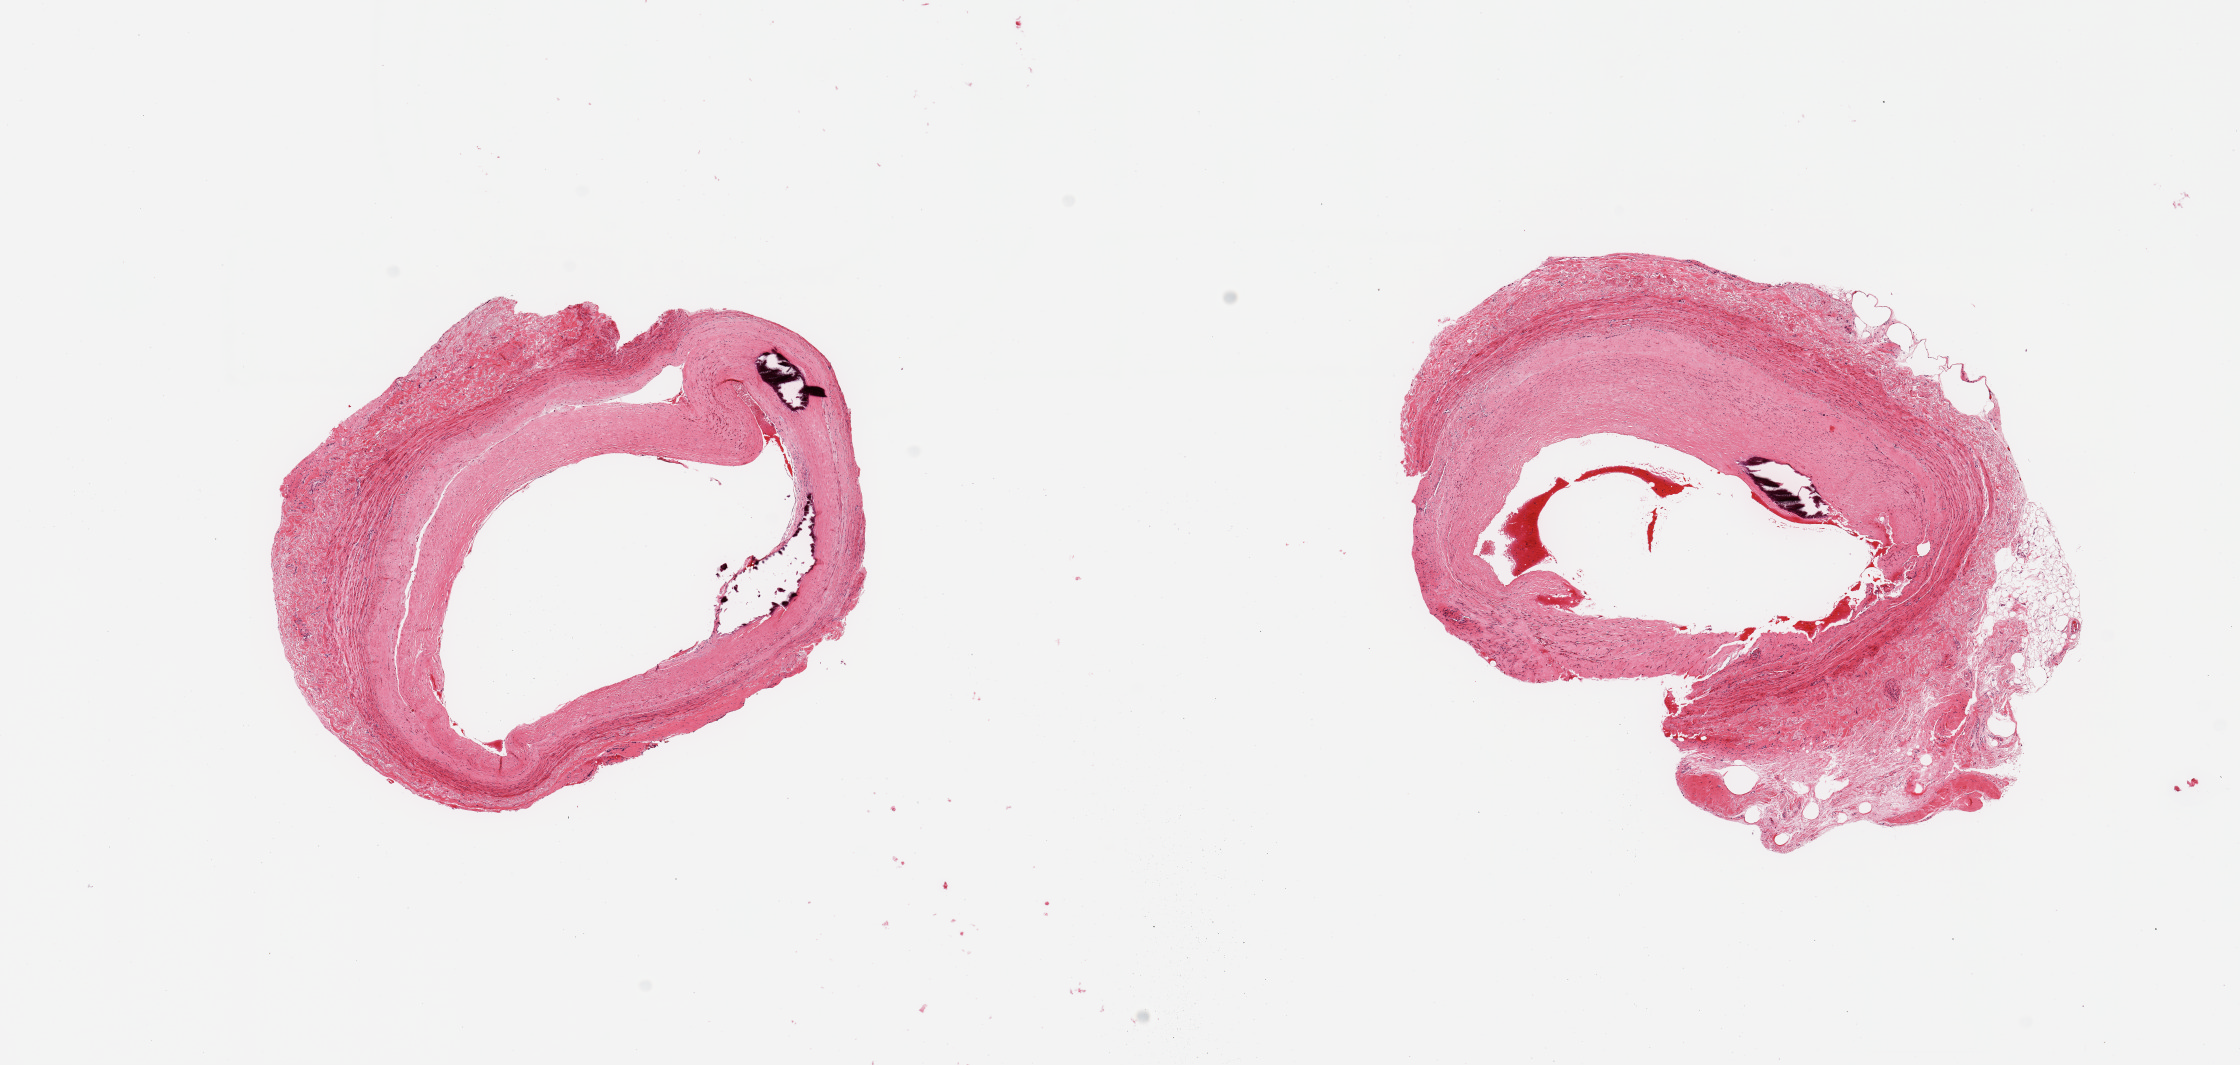
Hematoxylin and eosin (H&E) whole-slide image, a low-resolution overview of the entire scanned area, about 17.7 x 8.4 mm; PAXgene-fixed paraffin-embedded (PFPE) section; sampled site (target tissue): coronary artery; donor tissue sample. Male donor.
Review note (as recorded): 2 pieces; calcifications; fibrosclerotic plaque with about 50% luminal compromise; up to ~0.5mm and 1.4mm of adventitia.